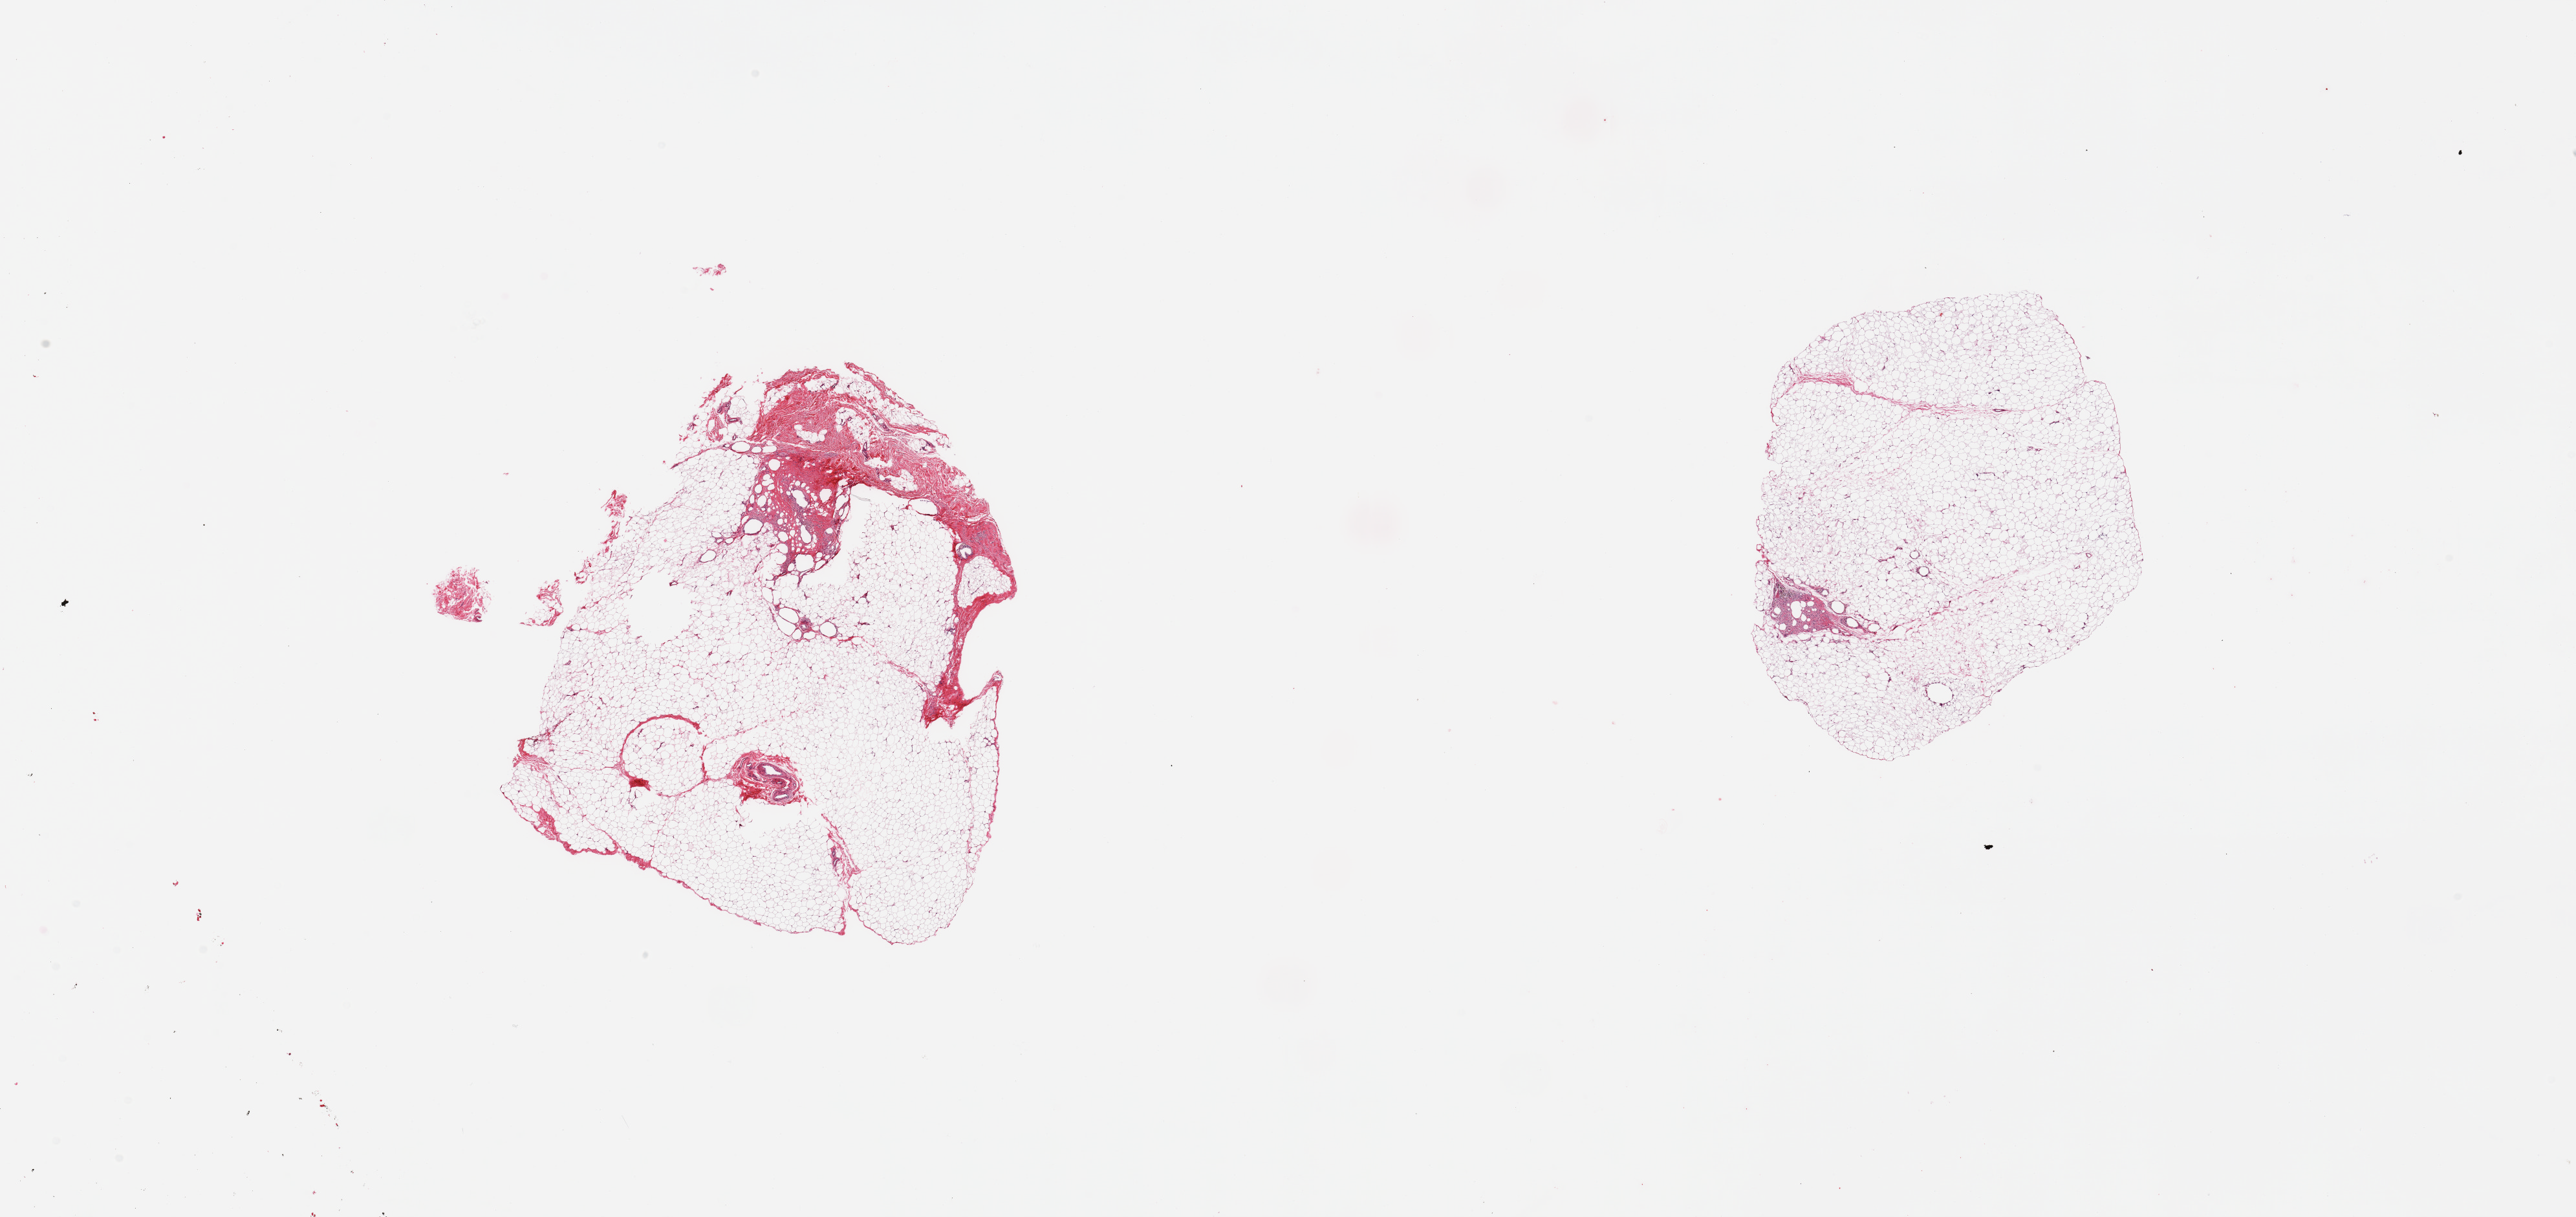
H&E whole-slide image, brightfield — low-resolution overview of the scanned area, about 31.5 x 14.9 mm, PAXgene-fixed, paraffin-embedded tissue, section of breast (target tissue), donor tissue sample. Male donor.
Review note (as recorded): 2 pieces; predominantly fat with small portion of stroma, focal macrophages/reactive changes/fat necrosis.